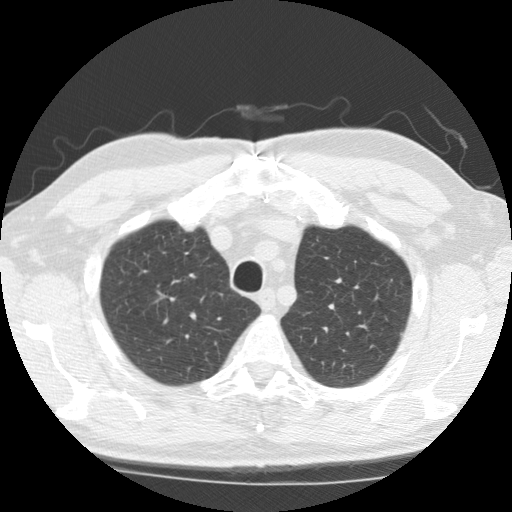
Low-dose screening chest CT, one axial slice; slice 155 of 196 in the series (ordered by position); reconstruction kernel STANDARD; lung window (W 1500 / L -600 HU); 2.5 mm slice thickness; 512 × 512 image matrix, field of view 350 × 350 mm.
Annotated regions visible in this slice (outlined manually by an expert reader):
- lesion 1 (tumor, upper lobe of right lung): box from (x=152, y=341) to (x=173, y=356) px